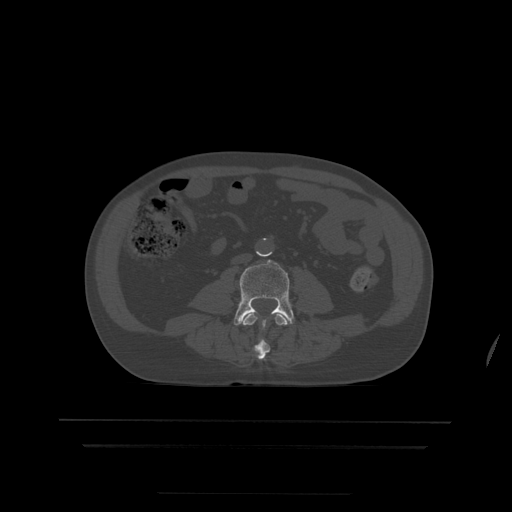
CT including the spine, one axial slice. Bone window (W 1800 / L 400 HU). 1.25 mm slice thickness. 512 × 512 image matrix, field of view 436 × 436 mm. Patient age 68 years. From the clinical record (not read from this slice): primary cancer: urothelial.
Structures marked on this image (semi-automatically segmented with operator editing):
- L3 vertebra: bounding box (x1, y1, x2, y2) in pixels: (241, 313, 291, 360)
- L4 vertebra: (234, 260, 295, 328)